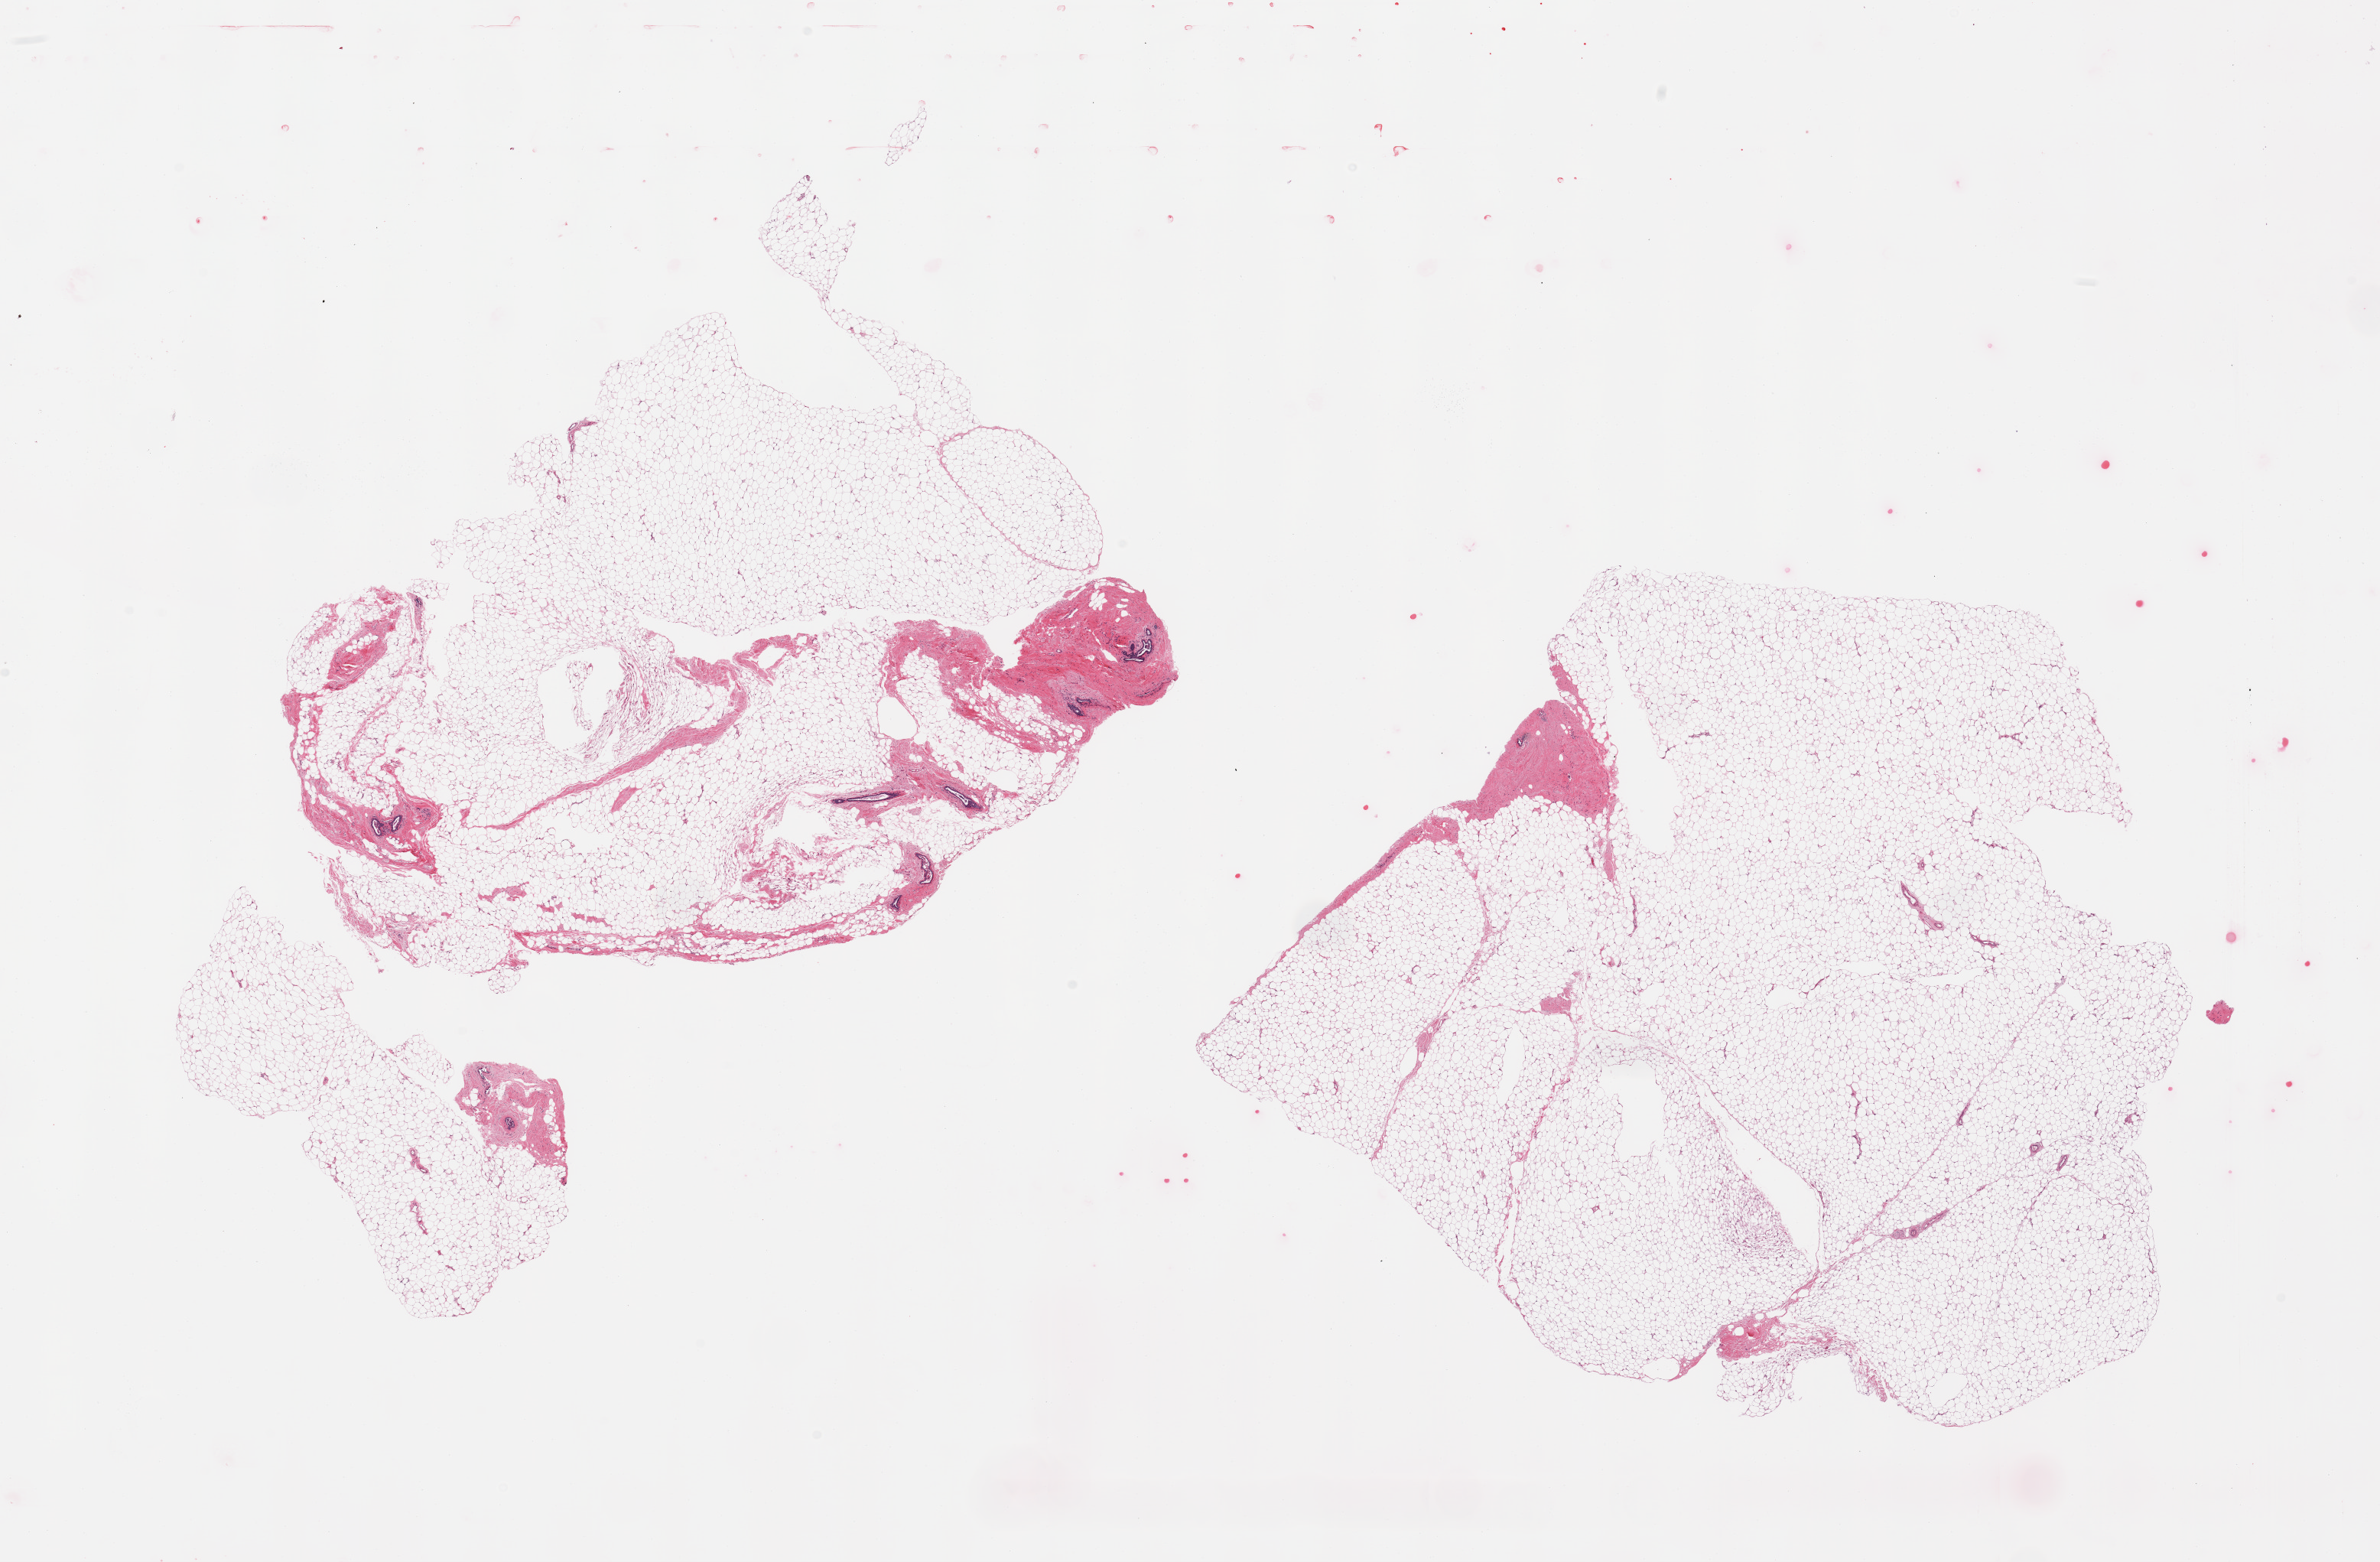
Whole-slide image, H&E stain — whole scanned area (about 24.6 x 16.1 mm) shown as a low-resolution overview, PAXgene-fixed, paraffin-embedded tissue, target tissue: breast, tissue donor sample. Female donor.
Reviewer comment on this tissue sample: 2 pieces; predominantly fat with up to ~10 and 20% fibrocollagenous tissue with benign ducts.